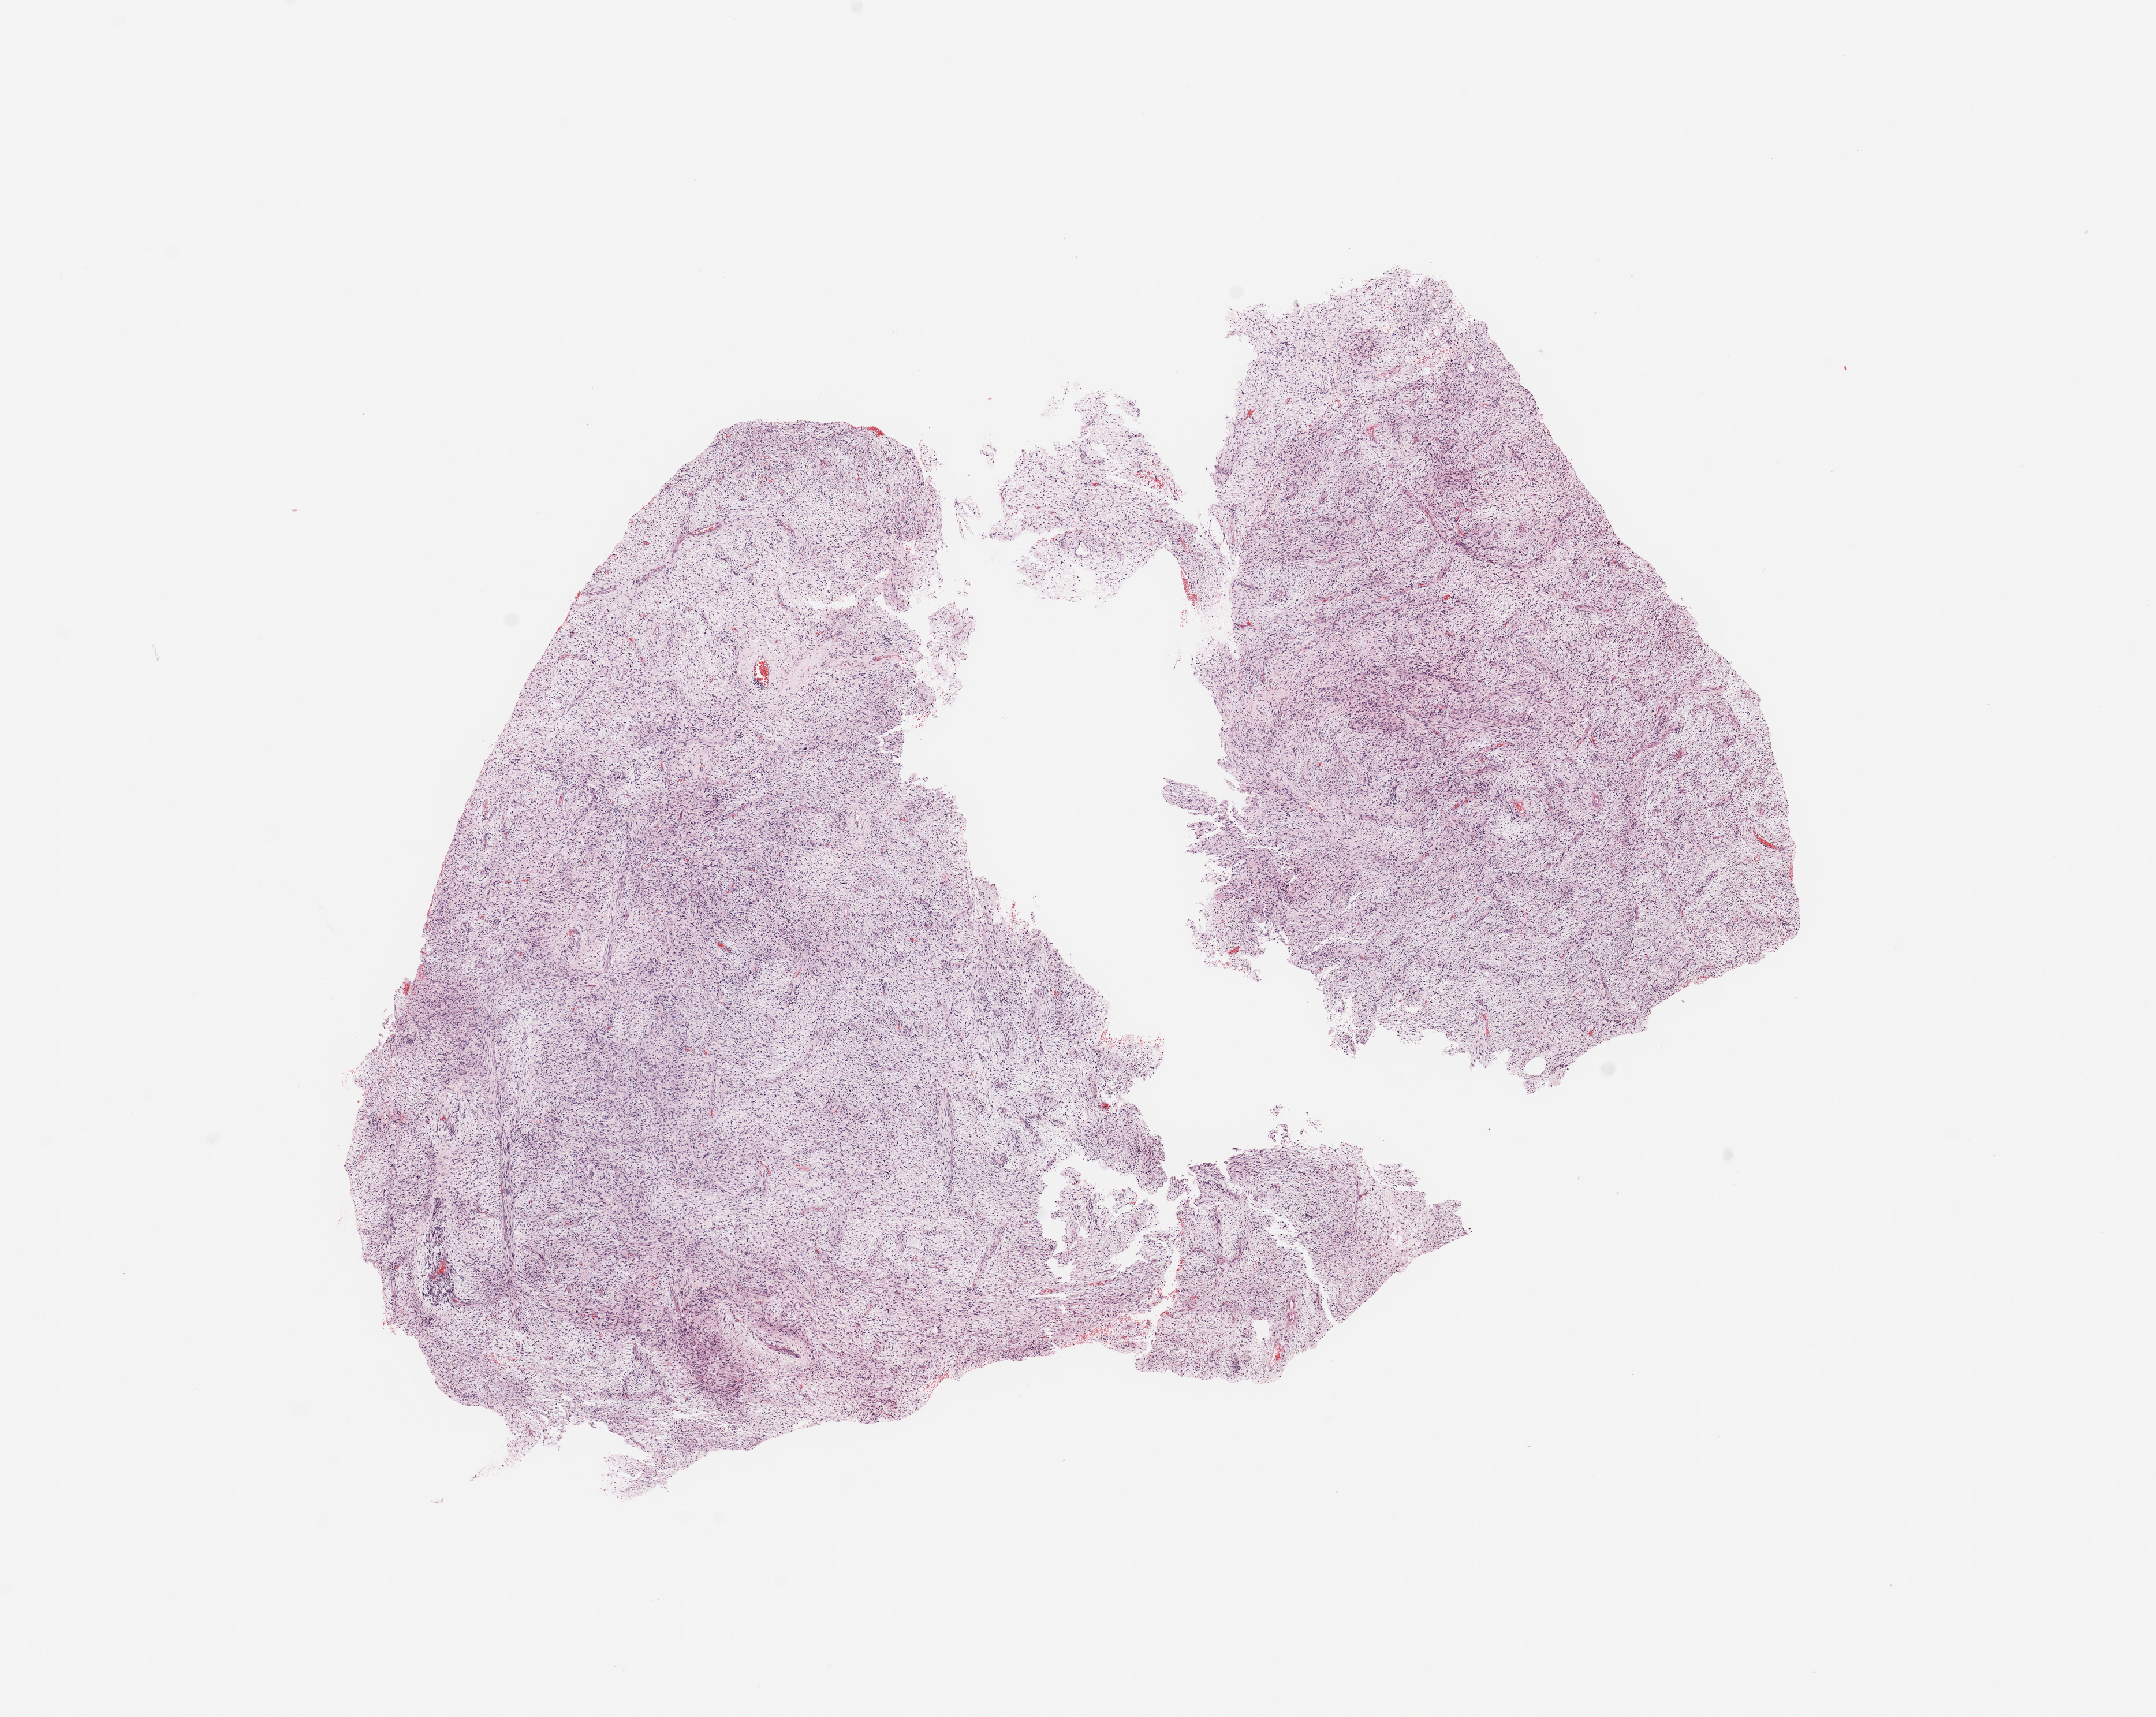
H&E whole-slide image — shown as a low-resolution overview of the whole scanned area (about 14.8 x 11.8 mm, acquisition: 20x scan). 66-year-old male patient.
- primary tumour site (as recorded): pelvic
- patient diagnosis (cohort enrolment): sarcoma (site not recorded at cohort level)